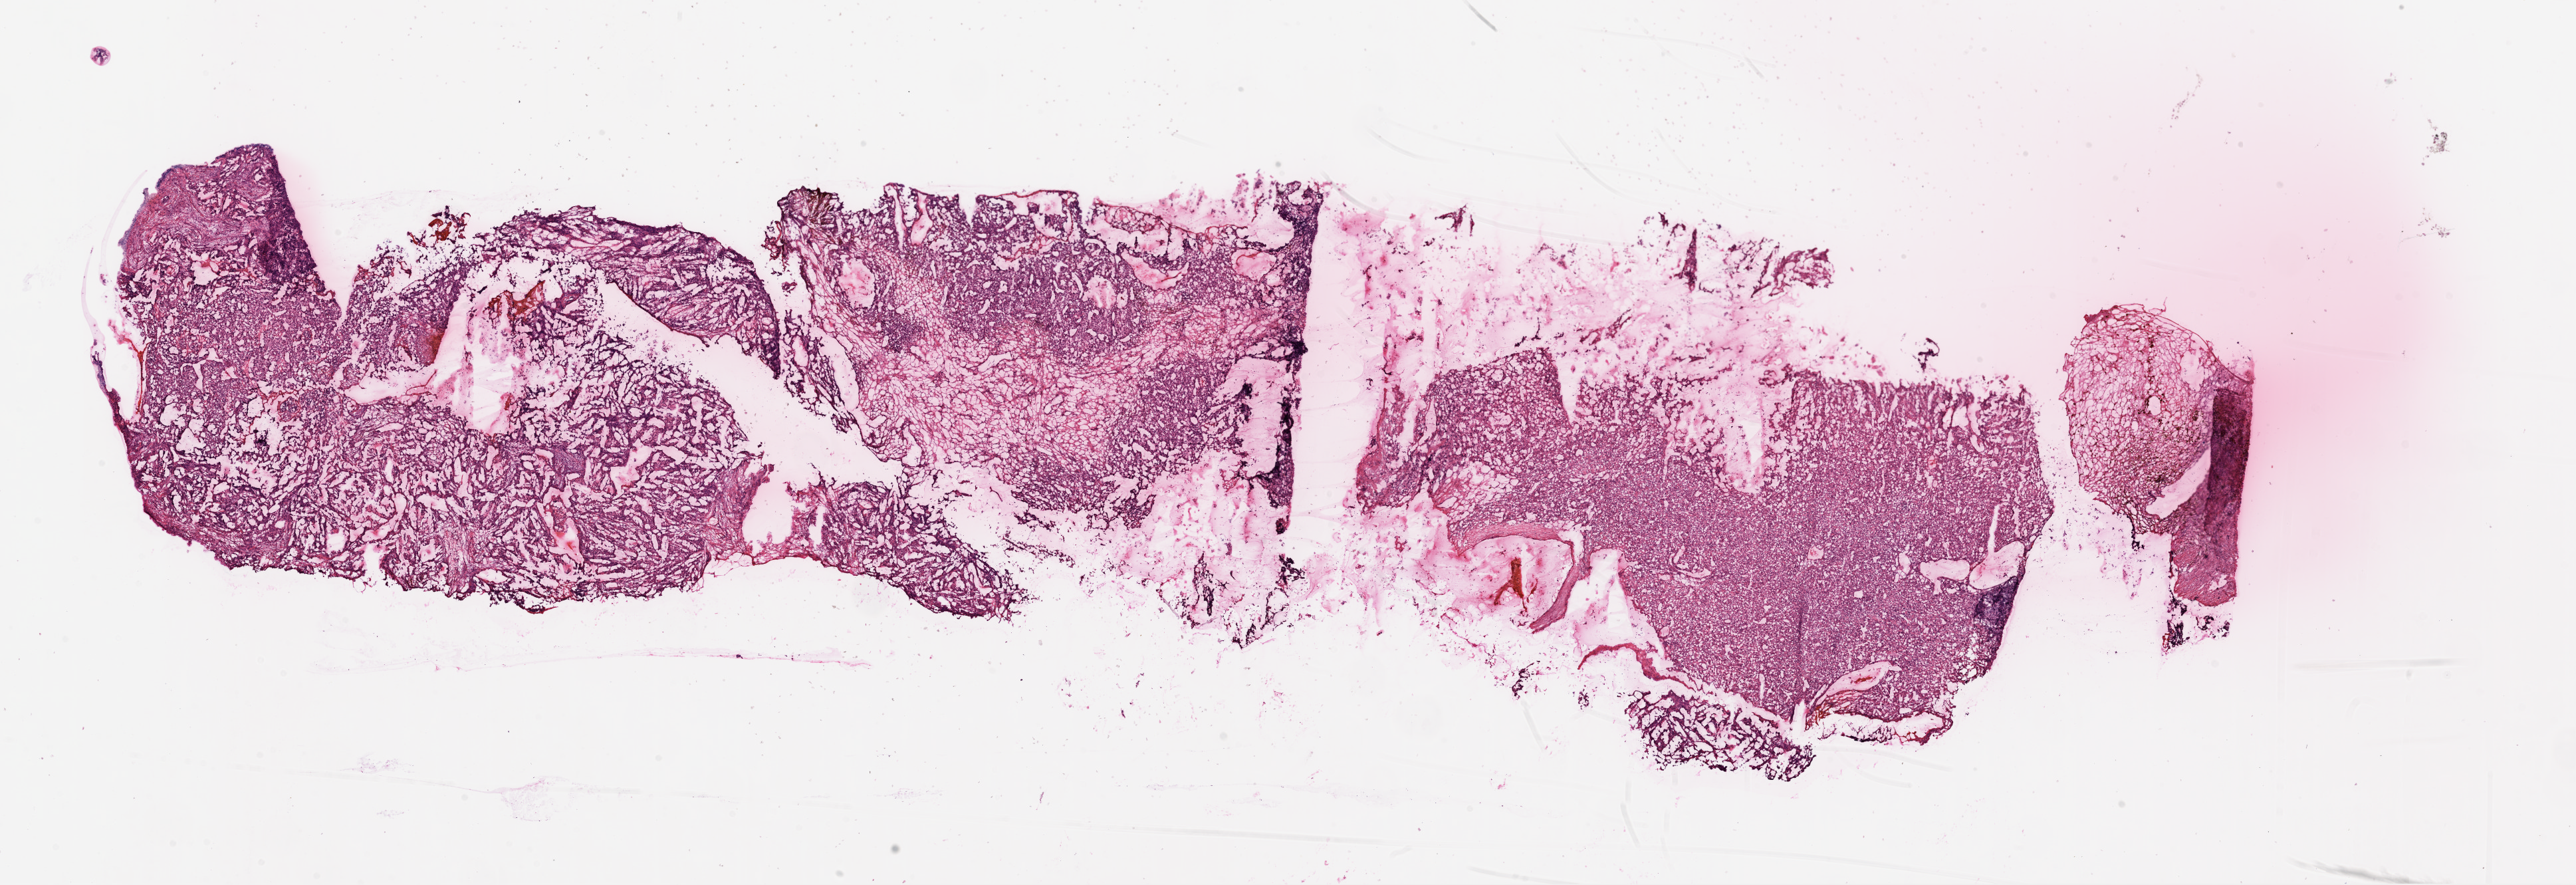
Whole-slide histology image, H&E-stained — low-resolution overview of the scanned area, about 31.1 x 10.7 mm (acquisition: 20x scan). Frozen section from the top of the tissue portion. Sample: primary tumour, kidney. Male, age 62 years at initial diagnosis. Slide review estimates, as recorded: tumour cells 90%, tumour nuclei 85%.
Diagnosis: Clear cell adenocarcinoma, NOS.